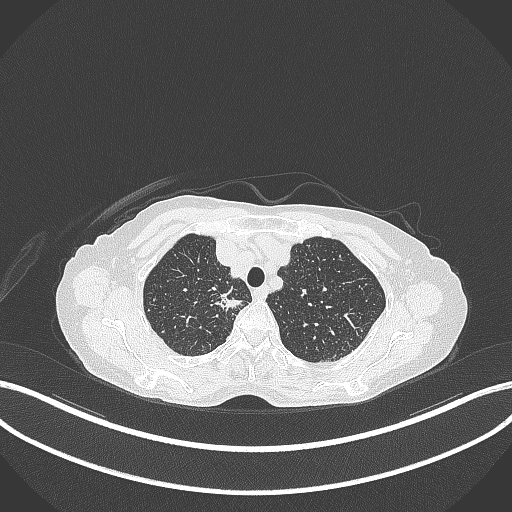
Chest CT, one axial slice. Slice 306 of 403 in the series (ordered by position). Reconstruction kernel B70f. 120 kVp. Lung window (W 1500 / L -600 HU). 1 mm slice thickness. 512 × 512 image matrix. Patient: female, 75 years. From the clinical record (not read from this slice): clinical TNM (as recorded): T1c N1 M1.
Structures marked on this image (rectangle marked by the reading radiologist):
- lung tumour (recorded histology: adenocarcinoma): box from (x=215, y=289) to (x=241, y=311) px